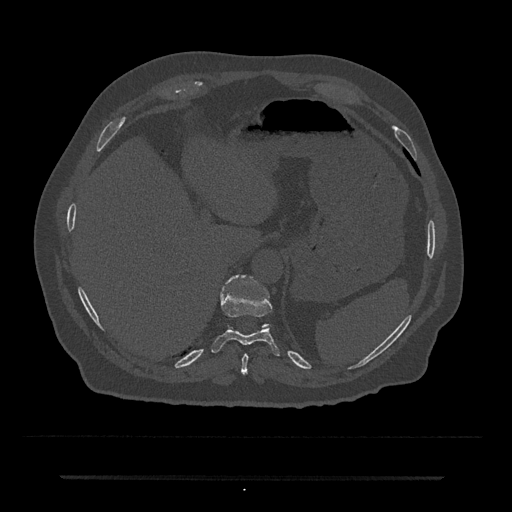
CT including the spine, one axial slice; slice 227 of 797 in the series (ordered by position); reconstruction kernel Br40s/3; 120 kVp; bone window (W 1800 / L 400 HU); 512 × 512 image matrix, field of view 437 × 437 mm. Patient: male, 69 years. From the clinical record (not read from this slice): primary cancer: prostate.
Outlined on this slice (semi-automatically segmented with operator editing):
- T10 vertebra: bounding box <211,275,280,356> (left, top, right, bottom; pixels)
- T11 vertebra: <224,275,268,327>
- T9 vertebra: <241,354,248,374>